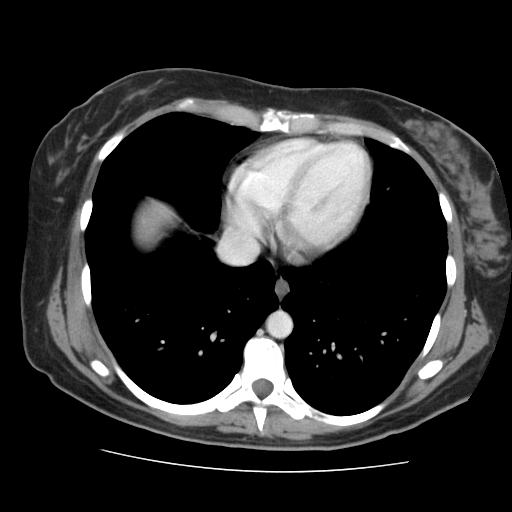
Contrast-enhanced abdominal CT, one axial slice. Position 140 of 144 along the scan axis. Soft-tissue window (W 400 / L 40 HU). 2.5 mm slice thickness. 512 × 512 image matrix, field of view 333 × 333 mm. Female patient, age 46 years. Case-level facts recorded for this patient, not image findings: diagnosis: colorectal cancer liver metastases, imaged before liver resection; multiple liver metastases: no; largest metastasis: 2.8 cm; chemotherapy before resection: yes.
Annotated regions visible in this slice (expert manual segmentation):
- hepatic veins: bounding box [x1, y1, x2, y2] px = [221, 239, 257, 264]